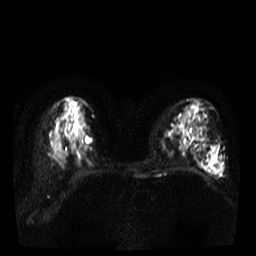
Breast MRI, one axial slice; slice 21 of 38 in the series (ordered by position); diffusion-weighted series; image 2 of 4 stored at this slice position (different b-values; order by instance number); 3 T; 5 mm slice thickness; 256 × 256 image matrix, field of view 320 × 320 mm. Female patient.
Structures marked on this image (expert manual segmentation):
- tumour on diffusion-weighted imaging: box from (x=210, y=159) to (x=221, y=172) px